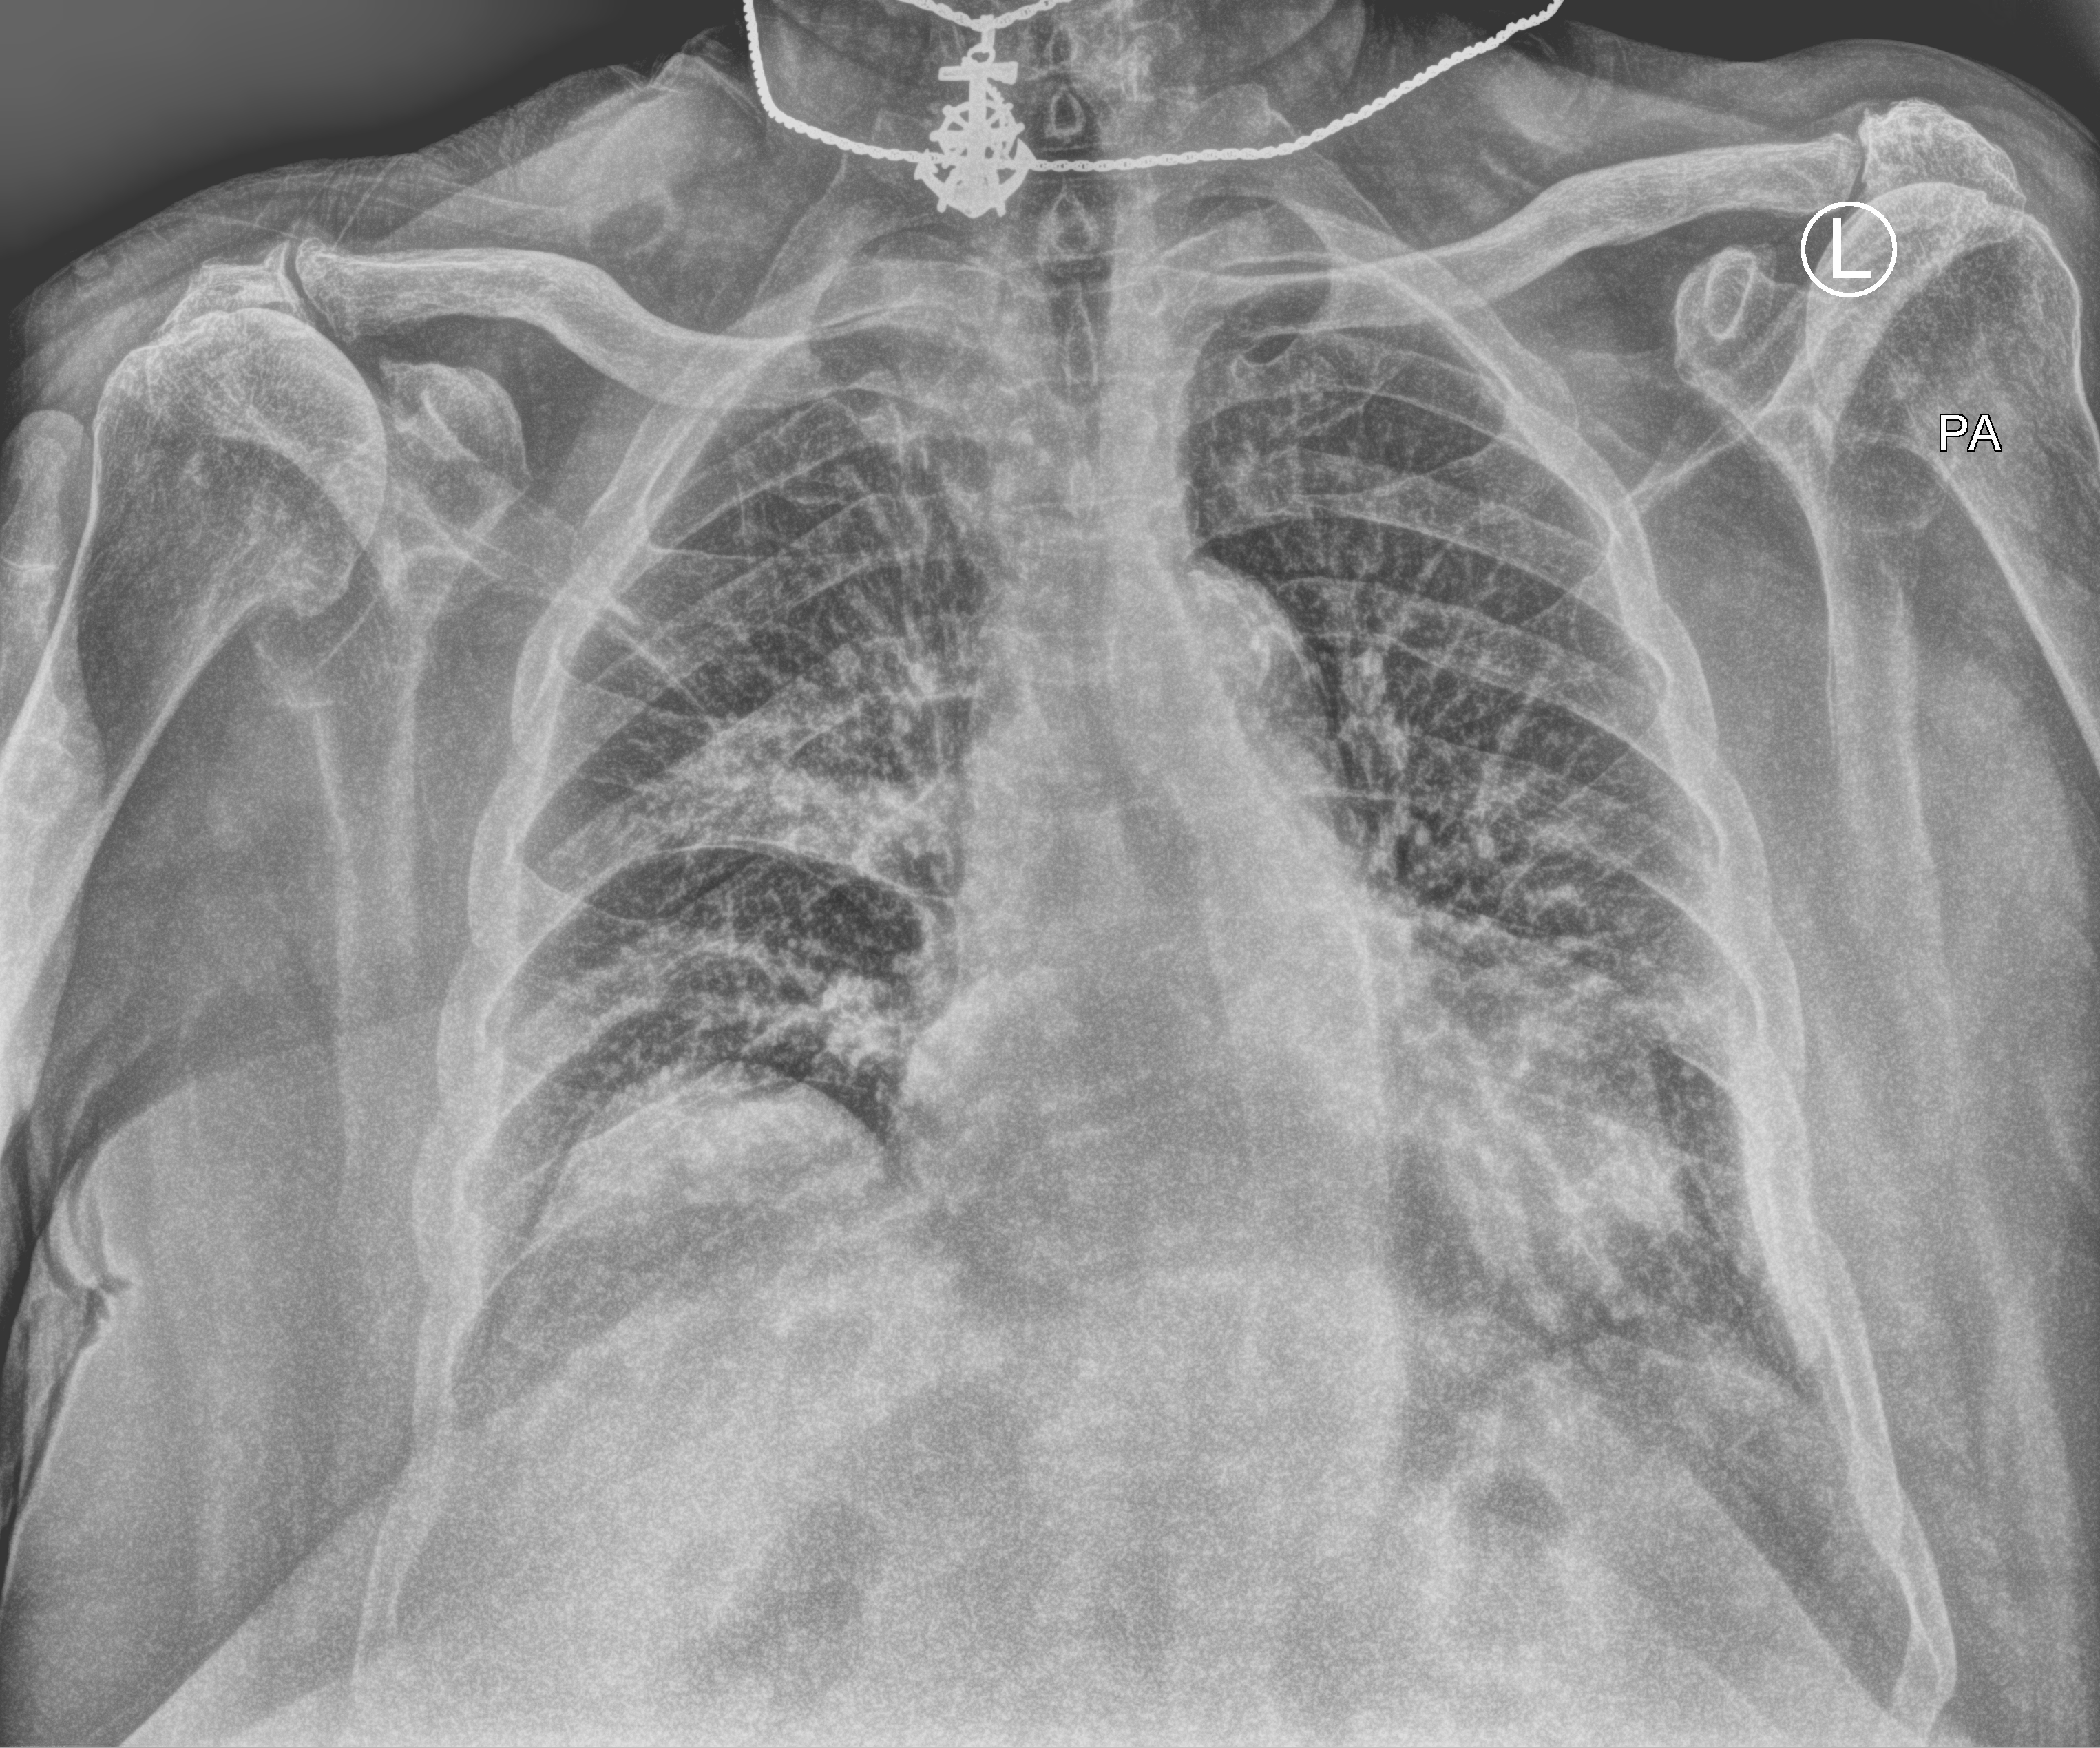
Bedside chest radiograph (computed radiography); anteroposterior (AP) projection. Male patient hospitalised with COVID-19, age 75–90 years.
Admission-level facts for this patient (not findings on this image; timing relative to this image not recorded): diabetes (admission record): no; admitted to intensive care during this hospital stay: no.